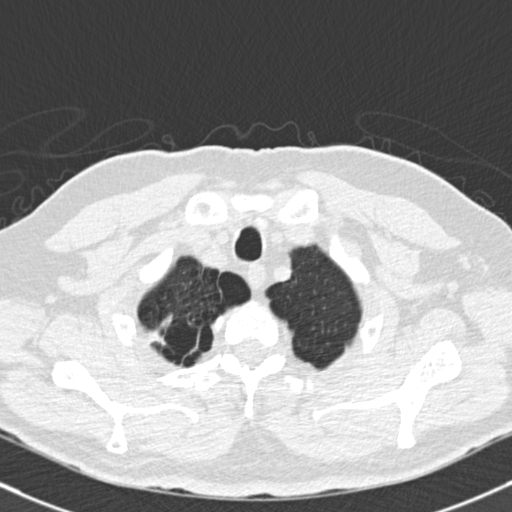
Low-dose screening chest CT, one axial slice. Position 148 of 165 along the scan axis. Reconstruction kernel B30f. 120 kVp. Lung window (W 1500 / L -600 HU). 2 mm slice thickness. 512 × 512 image matrix, field of view 324 × 324 mm.
Outlined on this slice (expert manual segmentation):
- lesion 1 (tumor, upper lobe of right lung): bounding box [x1, y1, x2, y2] px = [149, 317, 172, 346]